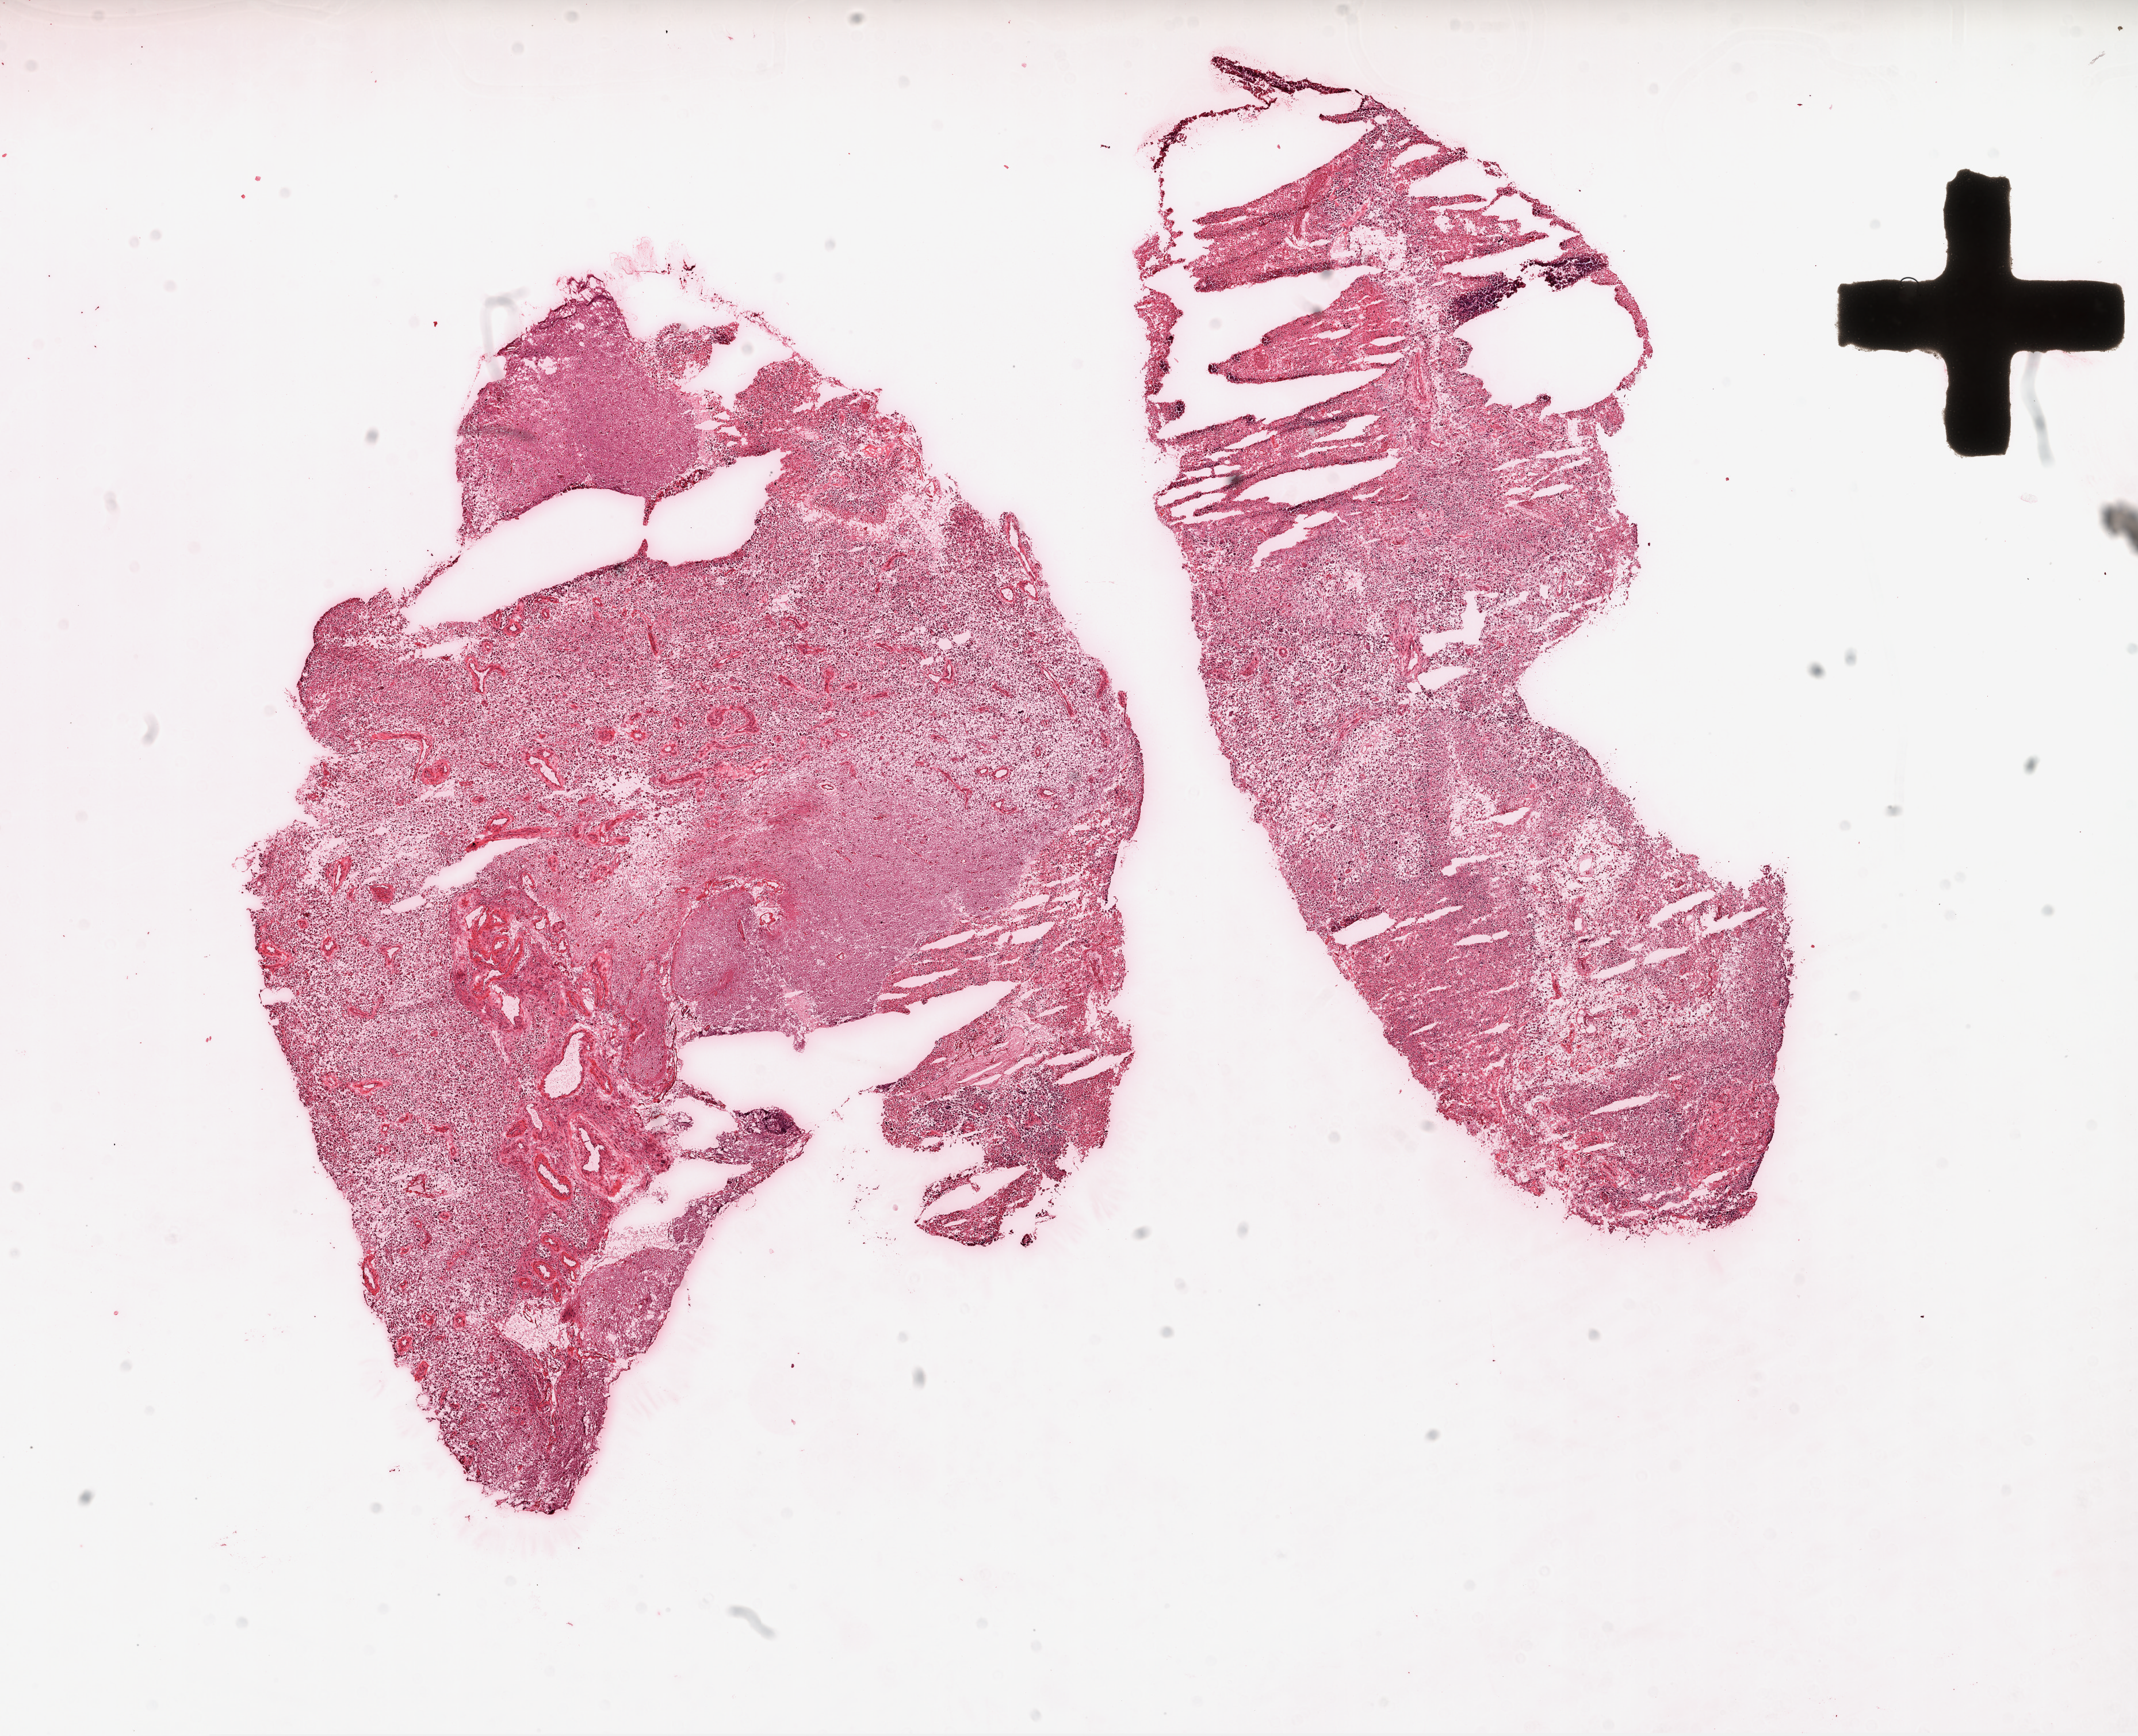
Whole-slide histology image, H&E-stained, shown as a low-resolution overview of the whole scanned area (about 15.0 x 12.2 mm); frozen section from the top of the tissue portion; sample: primary tumour, brain. Patient: male, age at initial diagnosis 67 years. Pathologist review of this section (percent, as recorded): tumour cells 75%, tumour nuclei 95%, normal cells 0%, stromal cells 20%, necrosis 5%.
* pathologic diagnosis: Glioblastoma